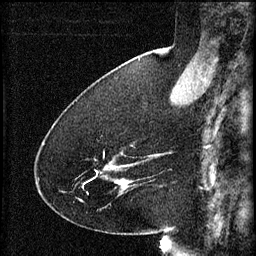
Breast MRI (dynamic contrast-enhanced), one sagittal slice; position 22 of 60 along the scan axis; 3 images stored at this slice position (order not interpretable as contrast timing); 1.5 T; TE 4.2 ms, TR 8.2 ms; 2 mm slice thickness; 256 × 256 image matrix, field of view 180 × 180 mm. Patient: female, 41 years.
Structures marked on this image (semi-automatic segmentation, software-assisted and operator-edited):
- analysis volume of interest (the breast-tissue region the enhancement analysis was run in; not a lesion): bounding box (x1, y1, x2, y2) in pixels: (78, 152, 134, 195)
- tumour enhancement mask (voxels above the 70 % enhancement threshold inside the analysis volume of interest): (117, 180, 128, 187)